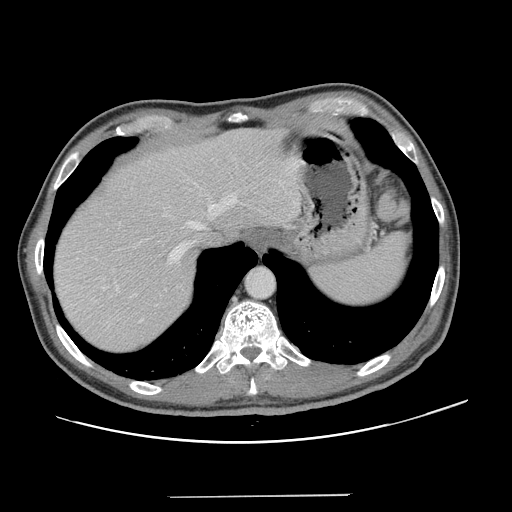
Contrast-enhanced abdominal CT, one axial slice. Slice 109 of 131 in the series (ordered by position). Intravenous contrast given. Soft-tissue window (W 400 / L 40 HU). 512 × 512 image matrix, field of view 403 × 403 mm. Male patient, age 60 years. From the clinical record (not read from this slice): diagnosis: colorectal cancer liver metastases, imaged before liver resection; multiple liver metastases: no; largest metastasis: 2.5 cm; disease in both lobes: no.
Structures marked on this image (manually delineated by an expert):
- hepatic veins: bounding box <162,193,238,272> (left, top, right, bottom; pixels)
- liver: <54,129,300,354>
- planned liver remnant (the part of the liver to remain after resection): <54,129,300,345>